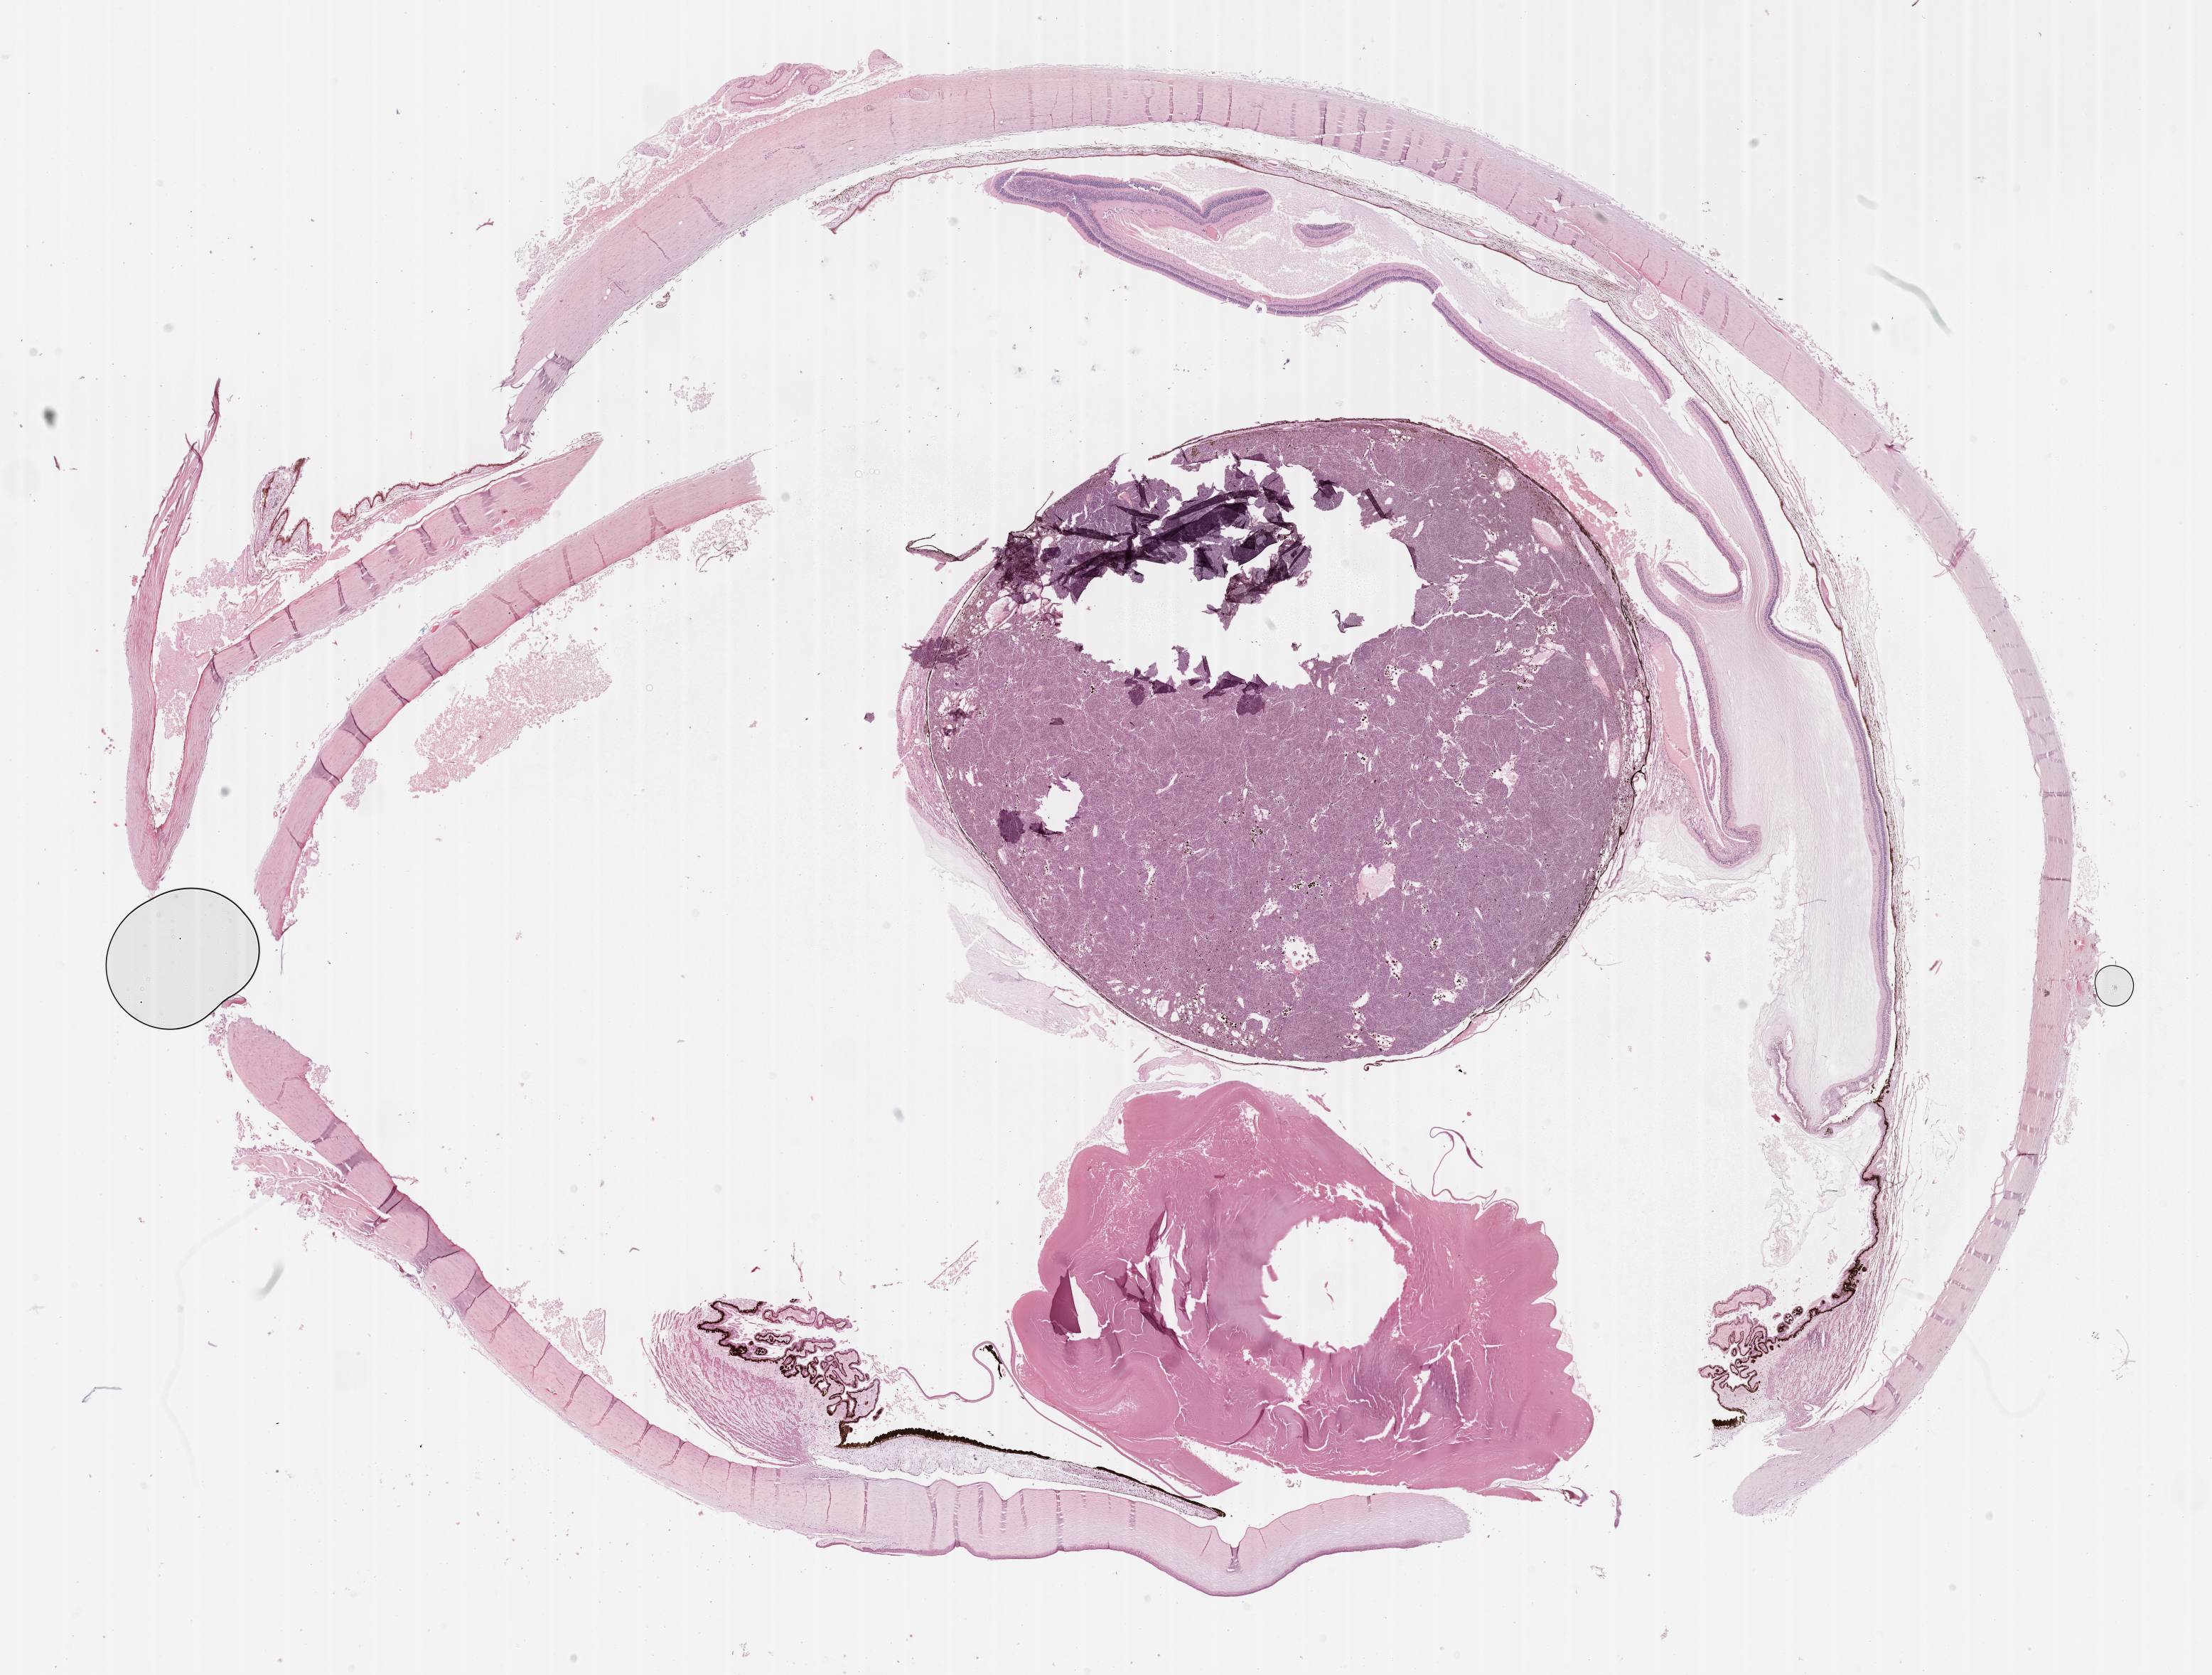
Whole-slide histology image, Hematoxylin and eosin (H&E) stained — a low-resolution overview of the entire scanned area, about 25.2 x 19.1 mm; formalin-fixed paraffin-embedded (FFPE) diagnostic section; primary tumour sample from the uvea. Female, age 66 years at initial diagnosis.
Diagnosis: Spindle cell melanoma, NOS (choroid).